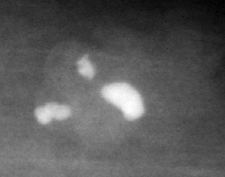
Crop from a digitized film mammogram around one marked abnormality, left breast, CC view.
- Marked abnormality: calcifications, morphology coarse; BI-RADS assessment category 2; subtlety rating 3 on a 1 (subtle) to 5 (obvious) scale; benign; no additional work-up was recommended (benign without callback).